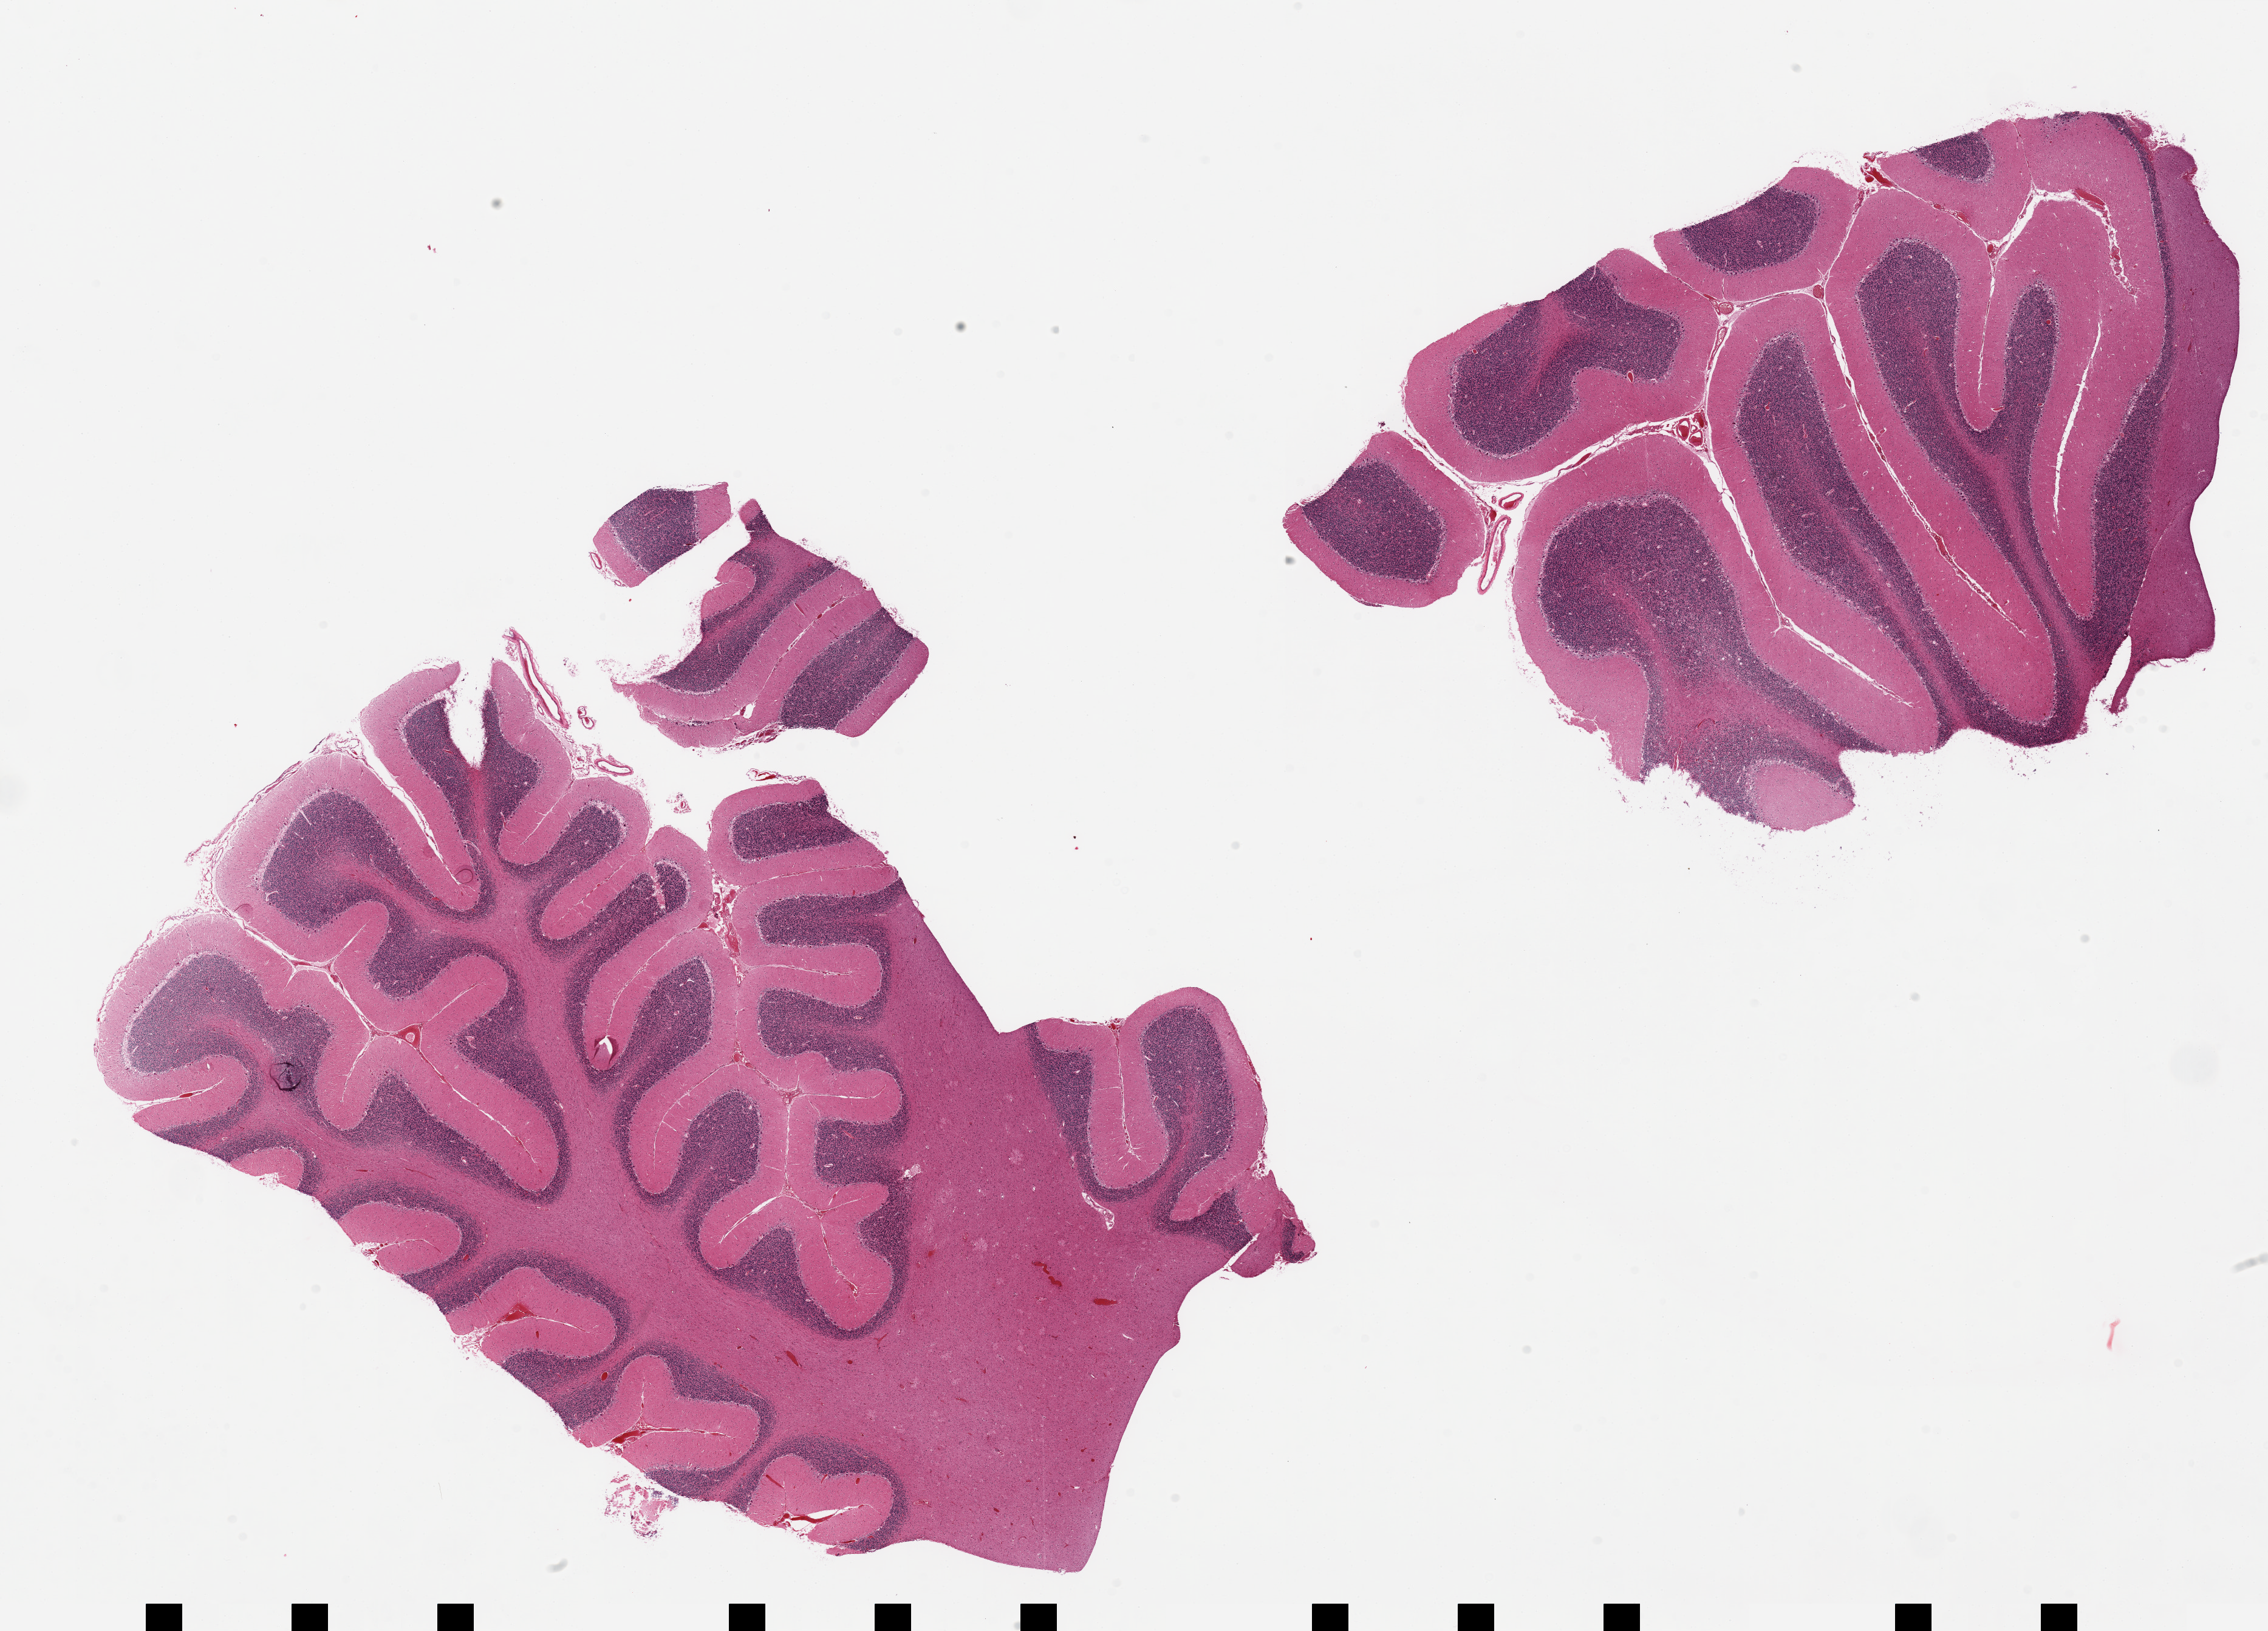
Digitized hematoxylin and eosin (H&E)-stained section, a low-resolution overview of the entire scanned area, about 29.5 x 21.2 mm (acquisition: 20x scan), PAXgene-fixed paraffin-embedded (PFPE) section, section of cerebellum (target tissue), tissue donor sample. Donor: male.
Review note (as recorded): 2 pieces; well preserved Purkinje cells.